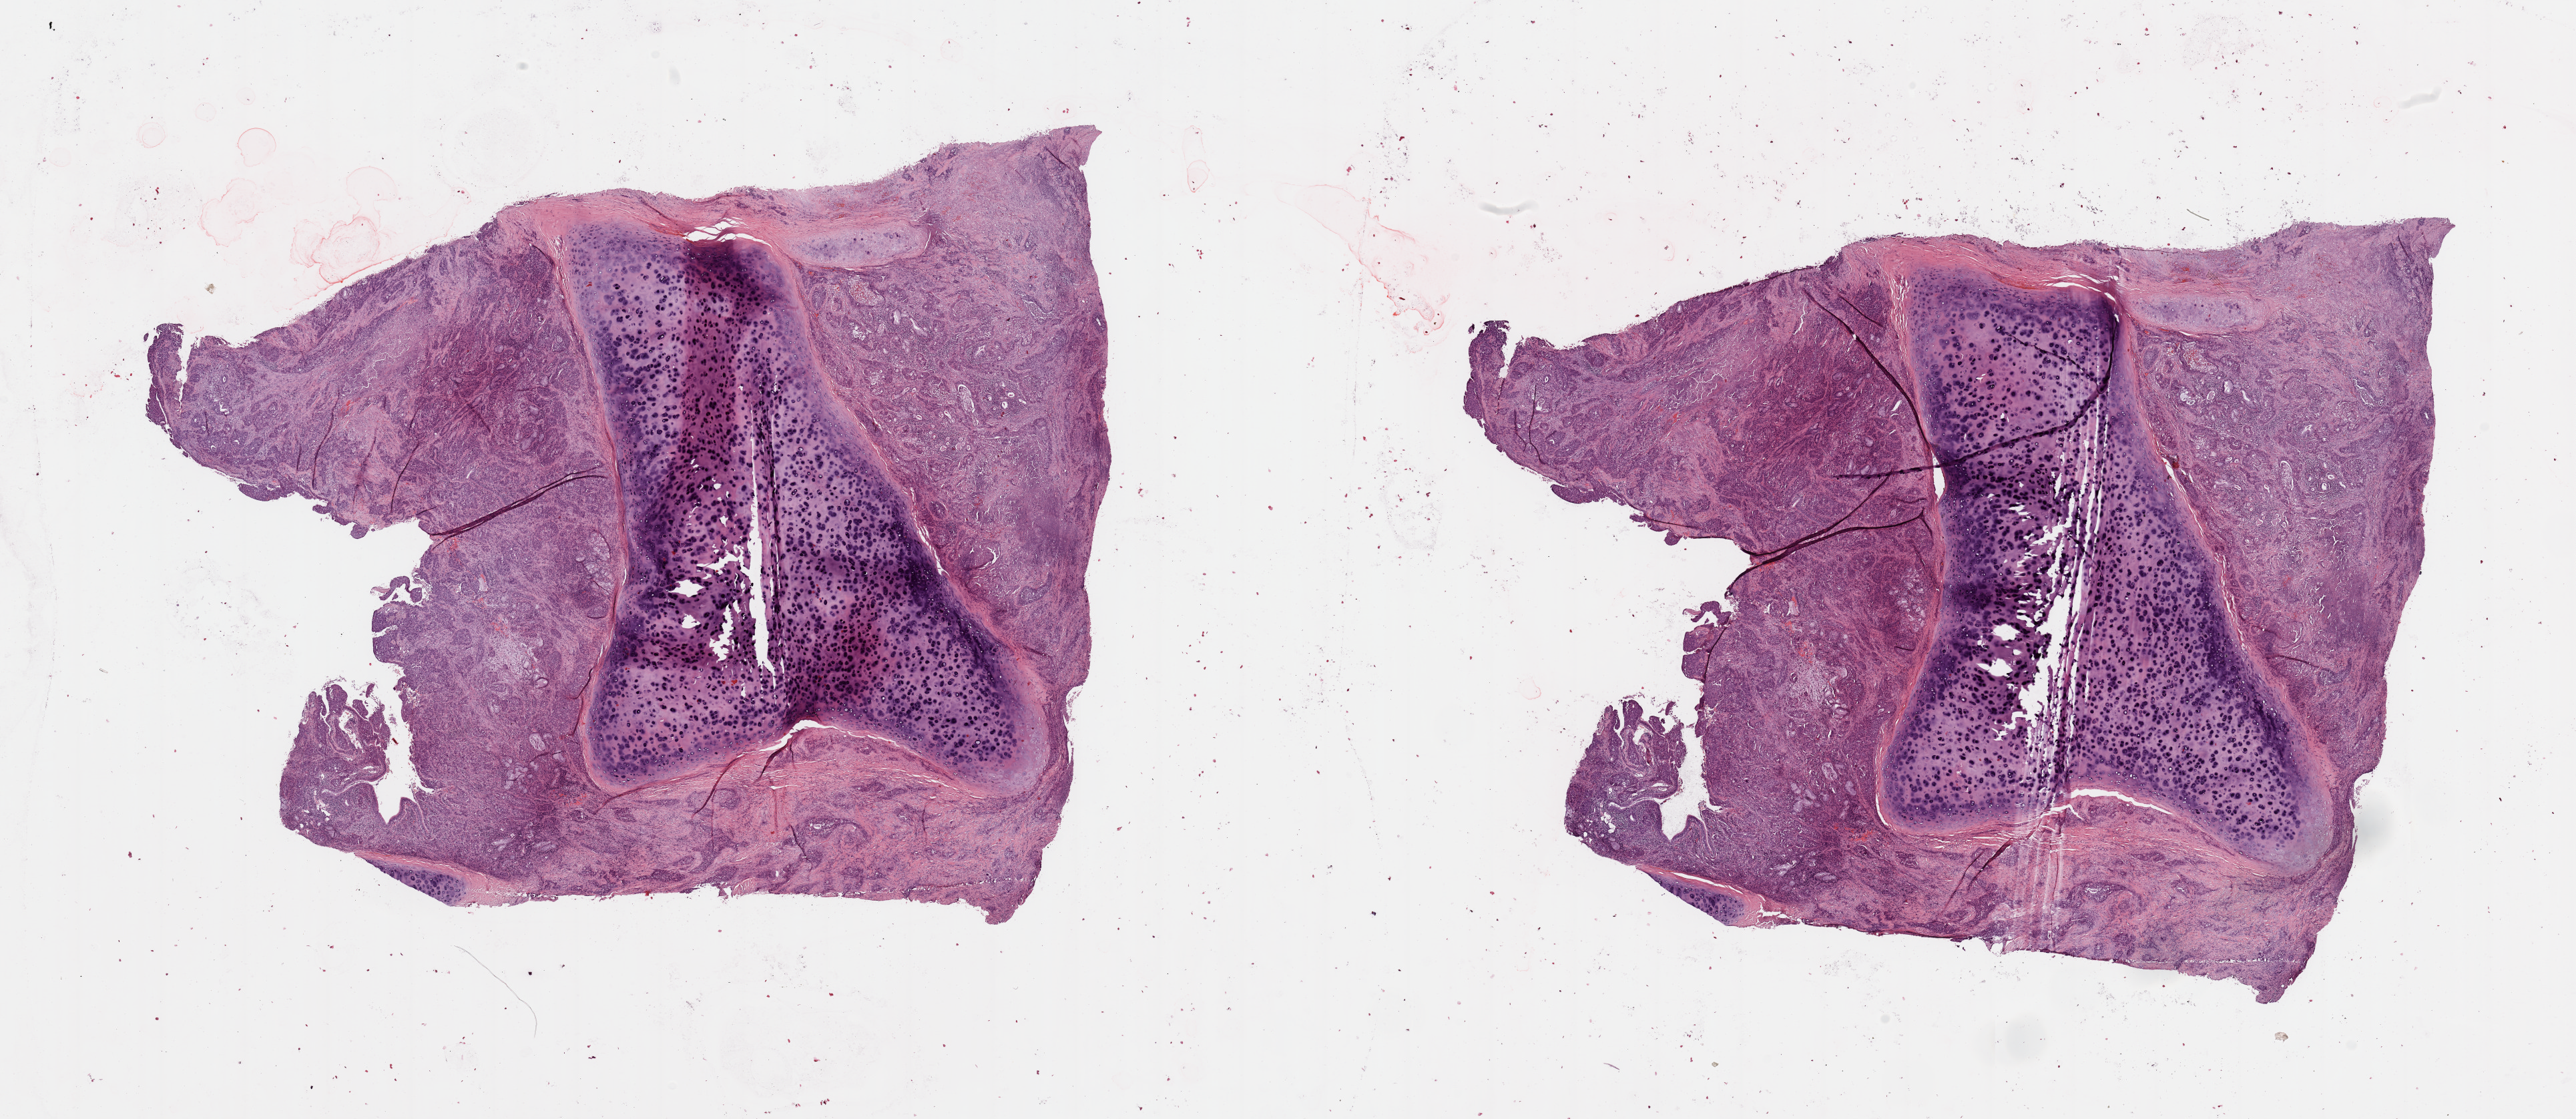
Whole-slide histology image, H&E — low-resolution overview of the scanned area, about 30.5 x 13.3 mm, tumour tissue sample, sampled site: lung. 72-year-old male patient. Histologic grade: G3 (poorly differentiated). Pathologist review of this section (percent, as recorded): tumour nuclei 55%, necrosis 10%.
Diagnosis: Squamous cell carcinoma, NOS. AJCC pathologic stage: IIA.